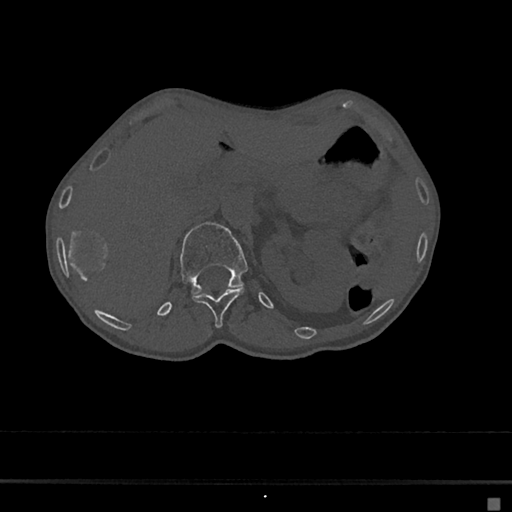
CT including the spine, one axial slice. Position 95 of 797 along the scan axis. Bone window (W 1800 / L 400 HU). 0.5 mm slice thickness. 512 × 512 image matrix, field of view 360 × 360 mm. Patient: female, 68 years. Case-level facts recorded for this patient, not image findings: primary cancer: renal.
Annotated regions visible in this slice (semi-automatically segmented with operator editing):
- L1 vertebra: bounding box (x1, y1, x2, y2) in pixels: (180, 222, 248, 295)
- T12 vertebra: (193, 288, 244, 328)